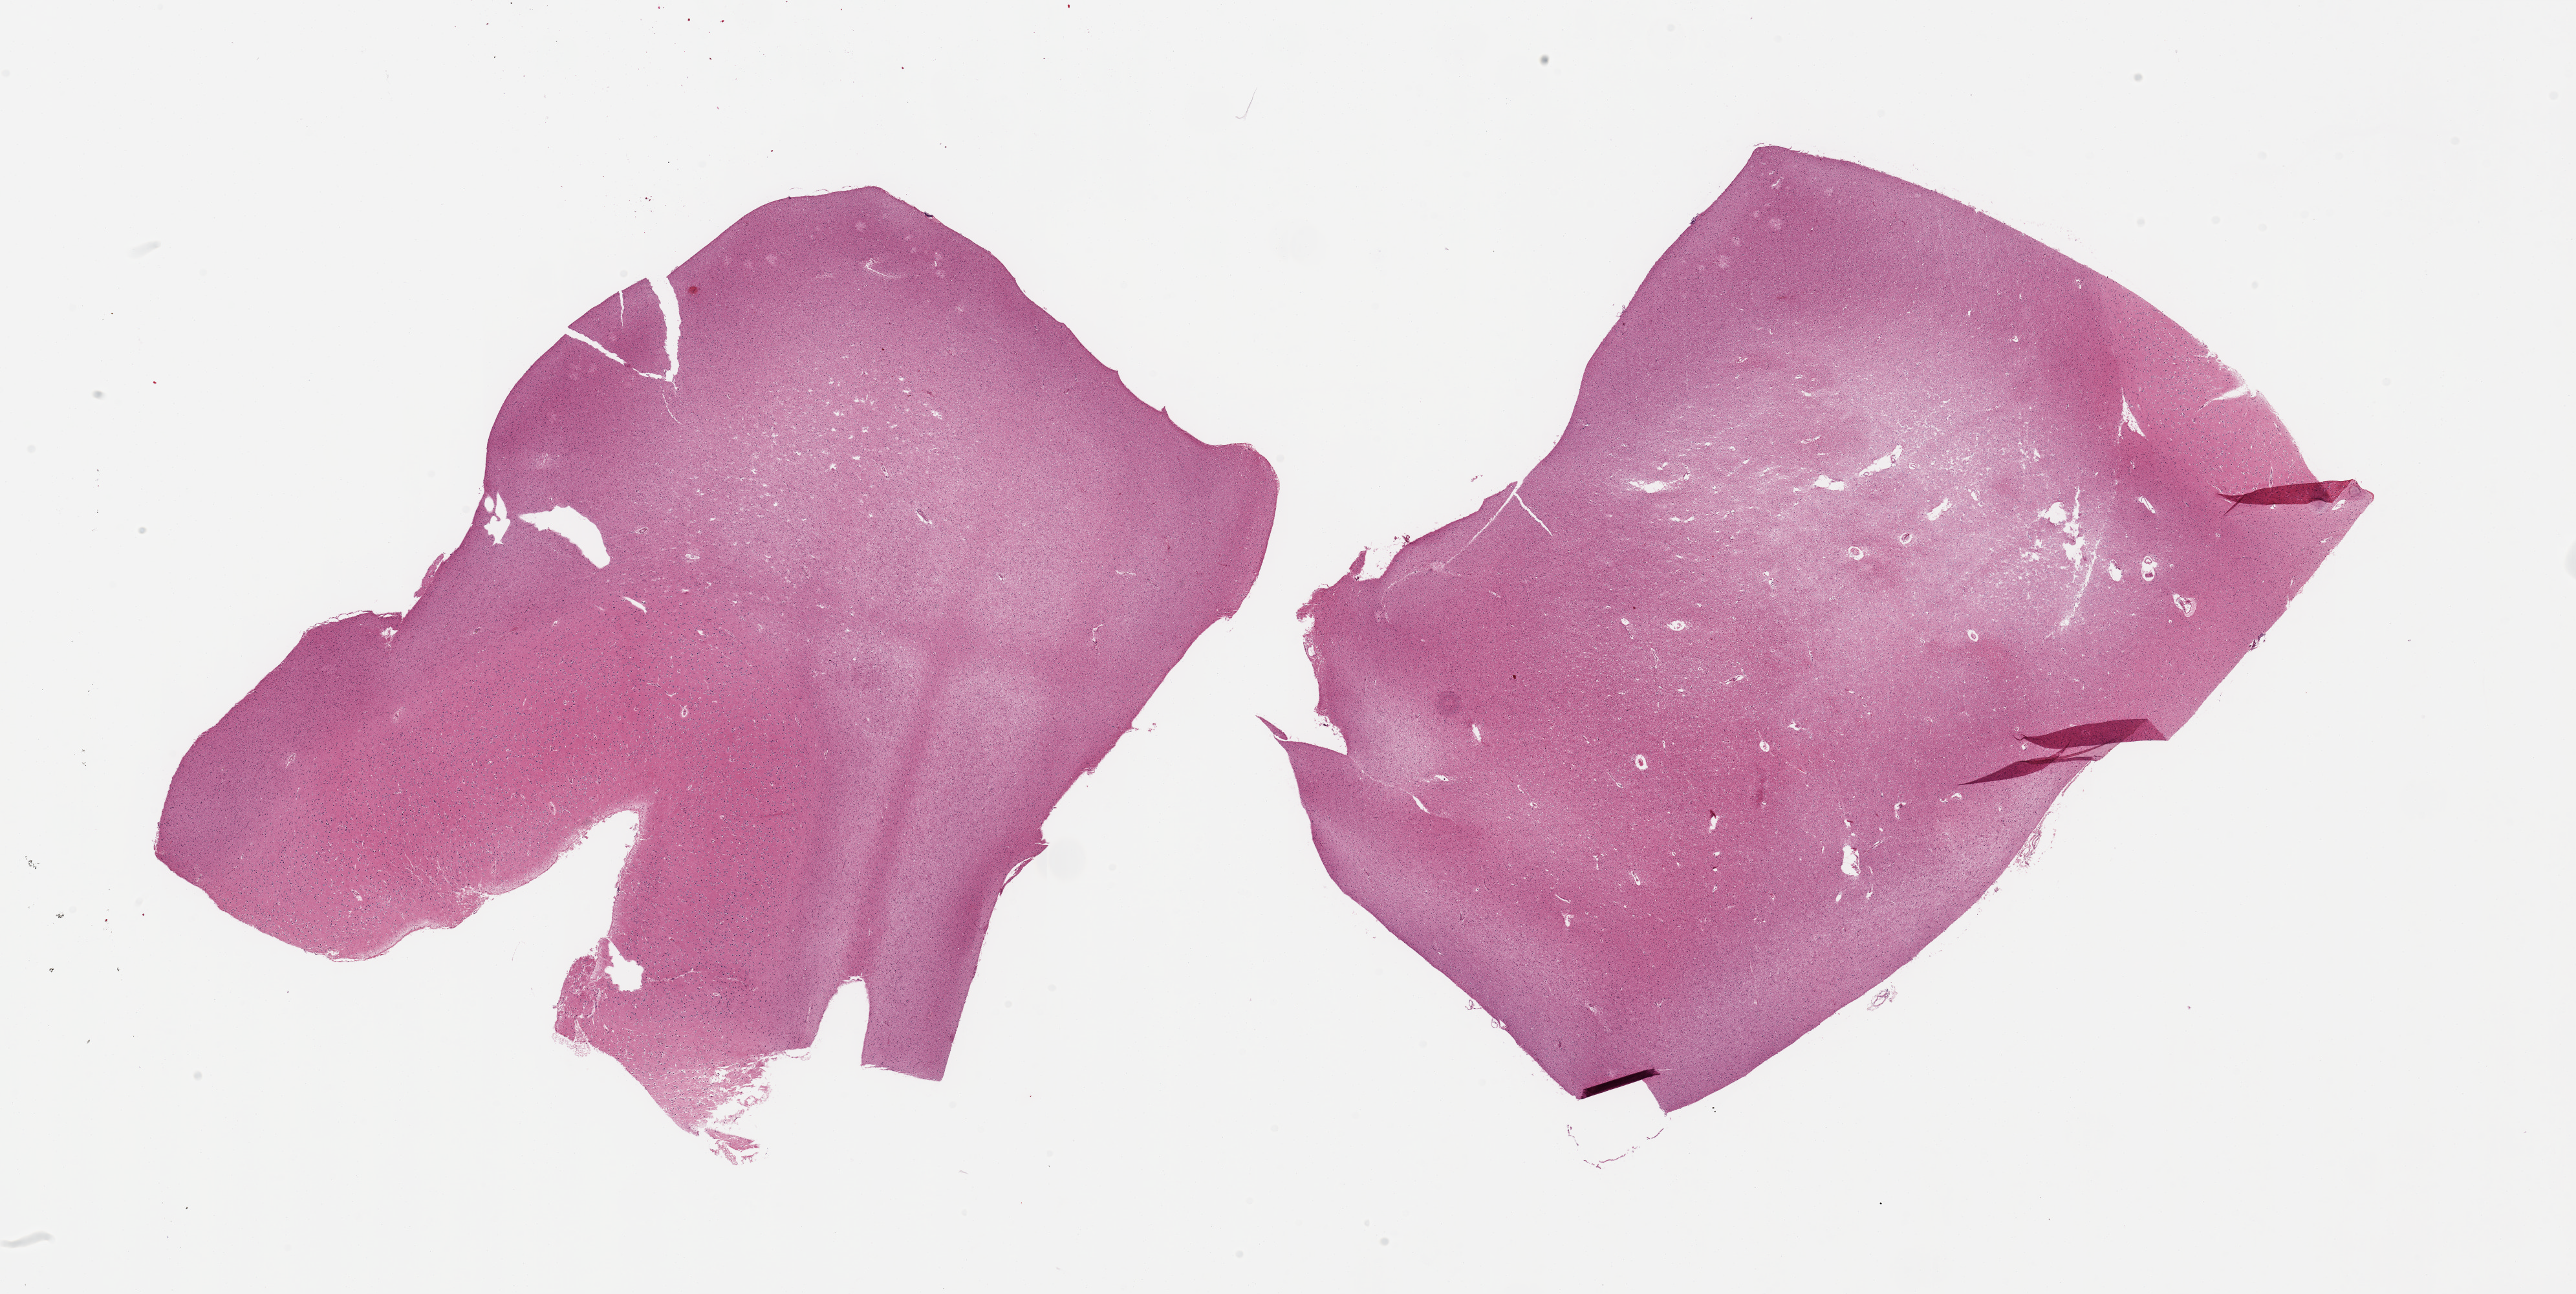
Digitized H&E-stained section — a low-resolution overview of the entire scanned area, about 31.5 x 15.8 mm, PAXgene-fixed, paraffin-embedded tissue, target tissue: cerebral cortex, tissue donor sample. Male donor.
Reviewer comment on this tissue sample: 2 pieces; more white matter than usual.